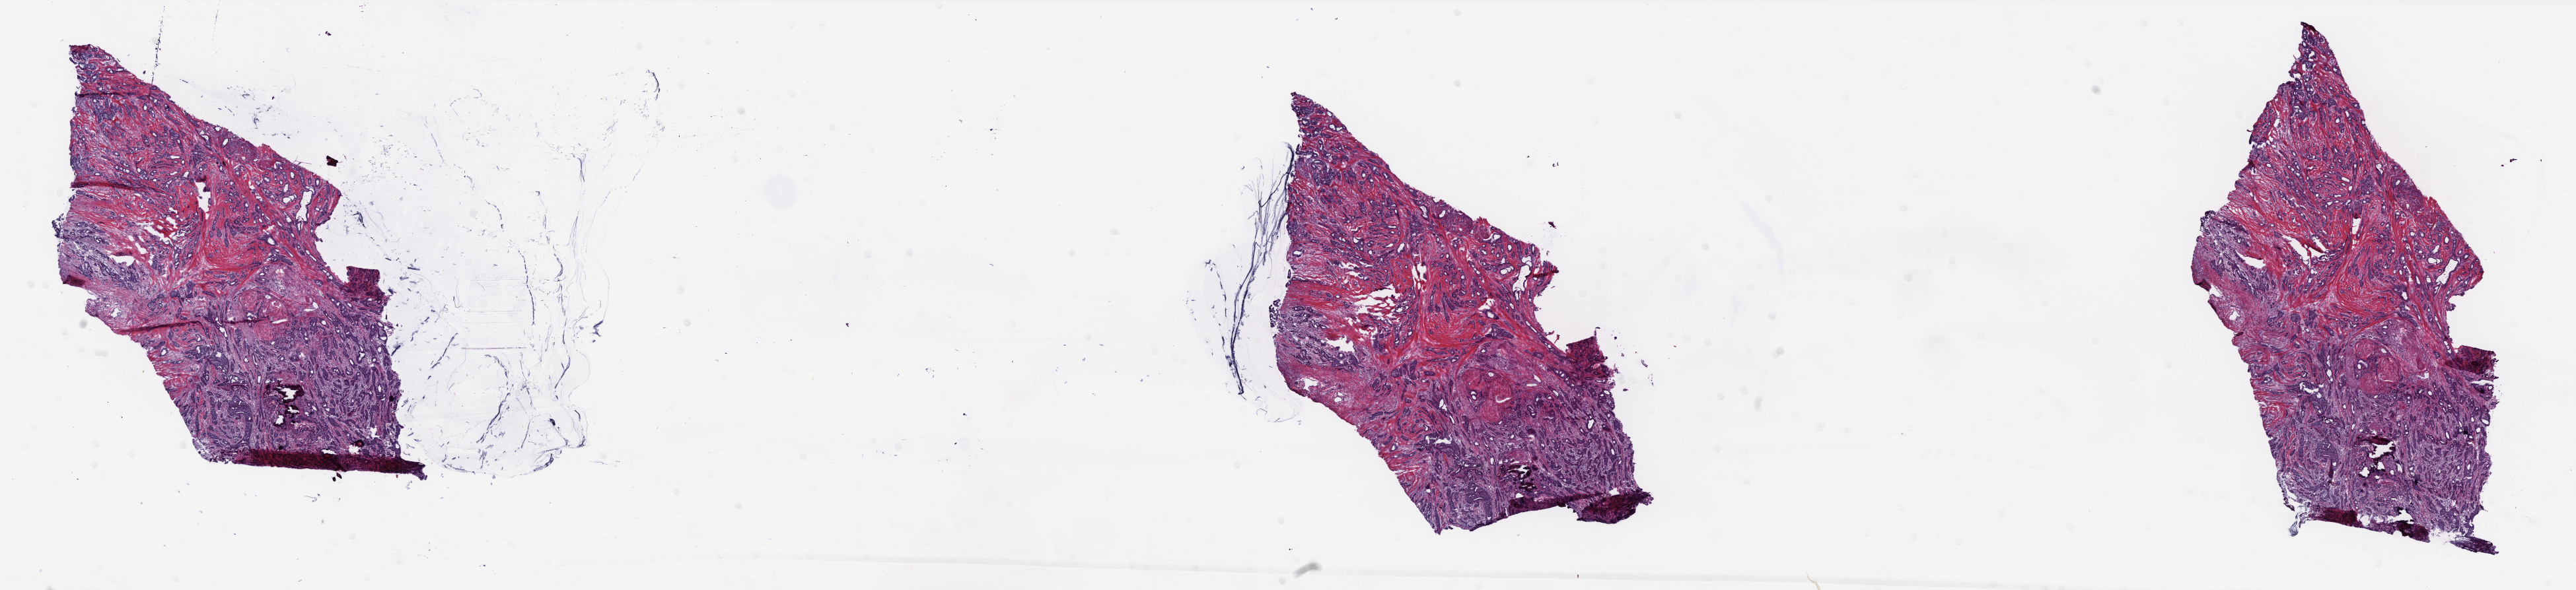
Digitized H&E-stained tissue section (whole slide), shown as a low-resolution overview of the whole scanned area (about 31.3 x 7.2 mm, from a 40x scan). Frozen section. Primary tumour sample from the breast. Patient: female, age at initial diagnosis 79 years. Slide review estimates, as recorded: tumour cells 70%, tumour nuclei 70%, normal cells 0%, stromal cells 27%, necrosis 3%. Infiltration values recorded for this section: lymphocyte infiltration 8%, monocyte infiltration 0%, neutrophil infiltration 0%.
Laterality: left. Lymph nodes positive (case pathology): 0 of 2 examined. Diagnosis: Infiltrating duct carcinoma, NOS. AJCC pathologic stage: IIA. TNM: T2 N0 (i-) M0.